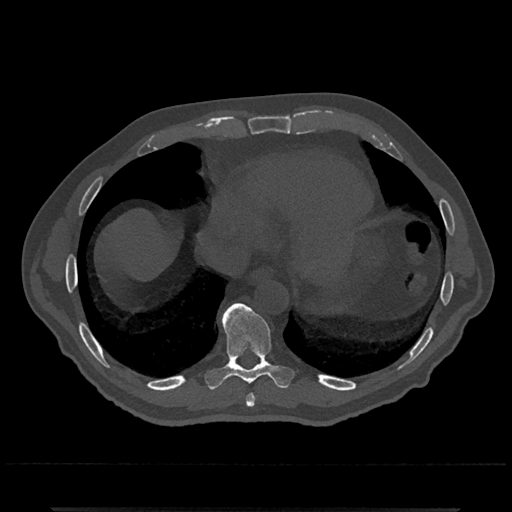
CT including the spine, one axial slice; position 614 of 797 along the scan axis; 120 kVp; bone window (W 1800 / L 400 HU); 512 × 512 image matrix, field of view 393 × 393 mm. Male patient, age 67 years. Case-level facts recorded for this patient, not image findings: primary cancer: prostate.
Annotated regions visible in this slice (semi-automatic segmentation, software-assisted and operator-edited):
- T8 vertebra: bounding box (x1, y1, x2, y2) in pixels: (246, 394, 255, 407)
- T9 vertebra: (205, 303, 294, 390)